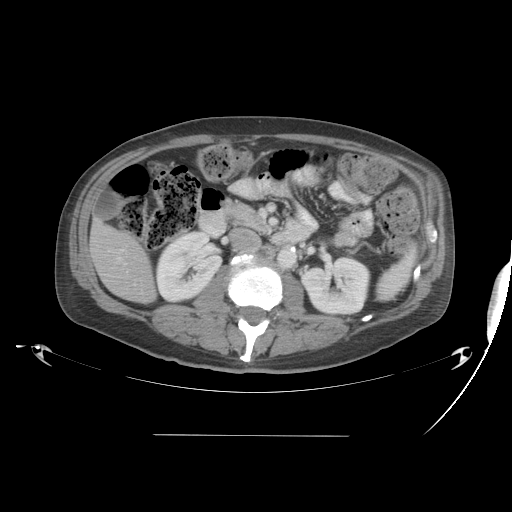
Contrast-enhanced abdominal CT, one axial slice. Position 16 of 48 along the scan axis. Reconstruction kernel STANDARD. 120 kVp. Intravenous contrast given. Soft-tissue window (W 400 / L 40 HU). 5 mm slice thickness. 512 × 512 image matrix, field of view 486 × 486 mm. Male patient, age 65 years. From the clinical record (not read from this slice): diagnosis: colorectal cancer liver metastases, imaged before liver resection; multiple liver metastases: yes; largest metastasis: 11 cm.
Structures marked on this image (manually delineated by an expert):
- liver: bounding box <91,222,156,304> (left, top, right, bottom; pixels)